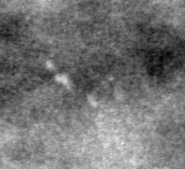
Crop from a digitized film mammogram around one marked abnormality, left breast, CC view, BI-RADS breast density category 4 (scale 1–4).
- Calcifications, morphology pleomorphic, distribution clustered; BI-RADS assessment category 4; pathology result (as recorded, not read from the image): benign.